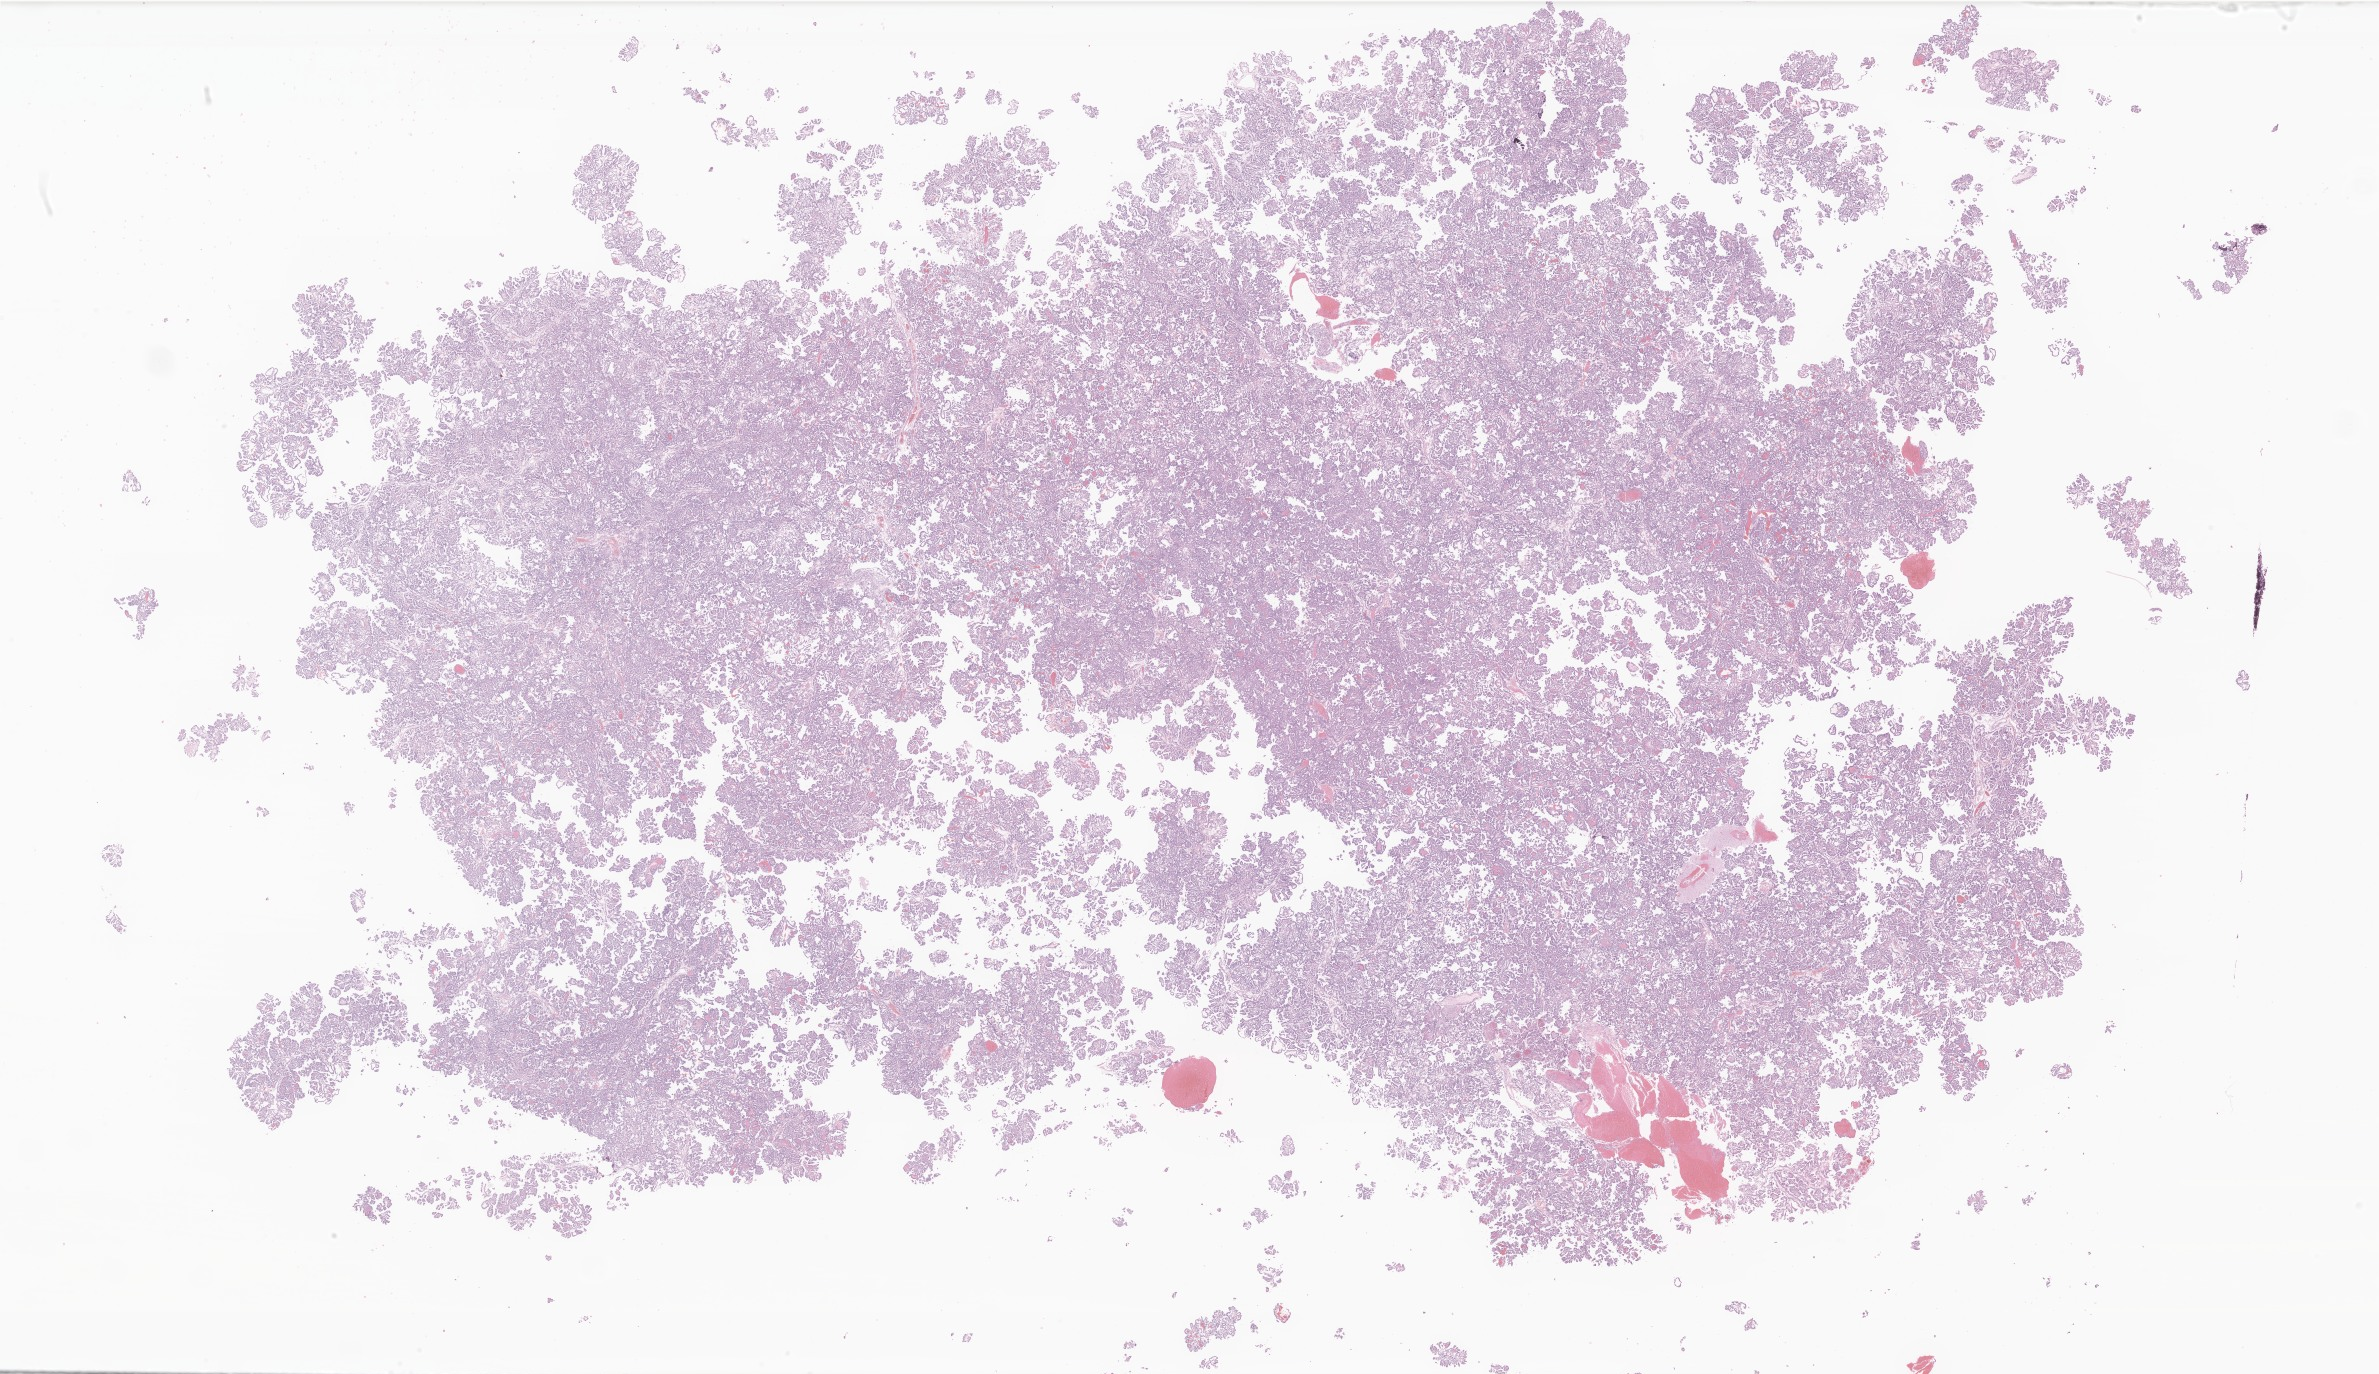
H&E whole-slide image of tumor tissue from the choroid of eye — whole scanned area (about 40.1 x 23.2 mm) shown as a low-resolution overview. FFPE section. Patient male; age 178 days.
* diagnosis: Atypical choroid plexus papilloma